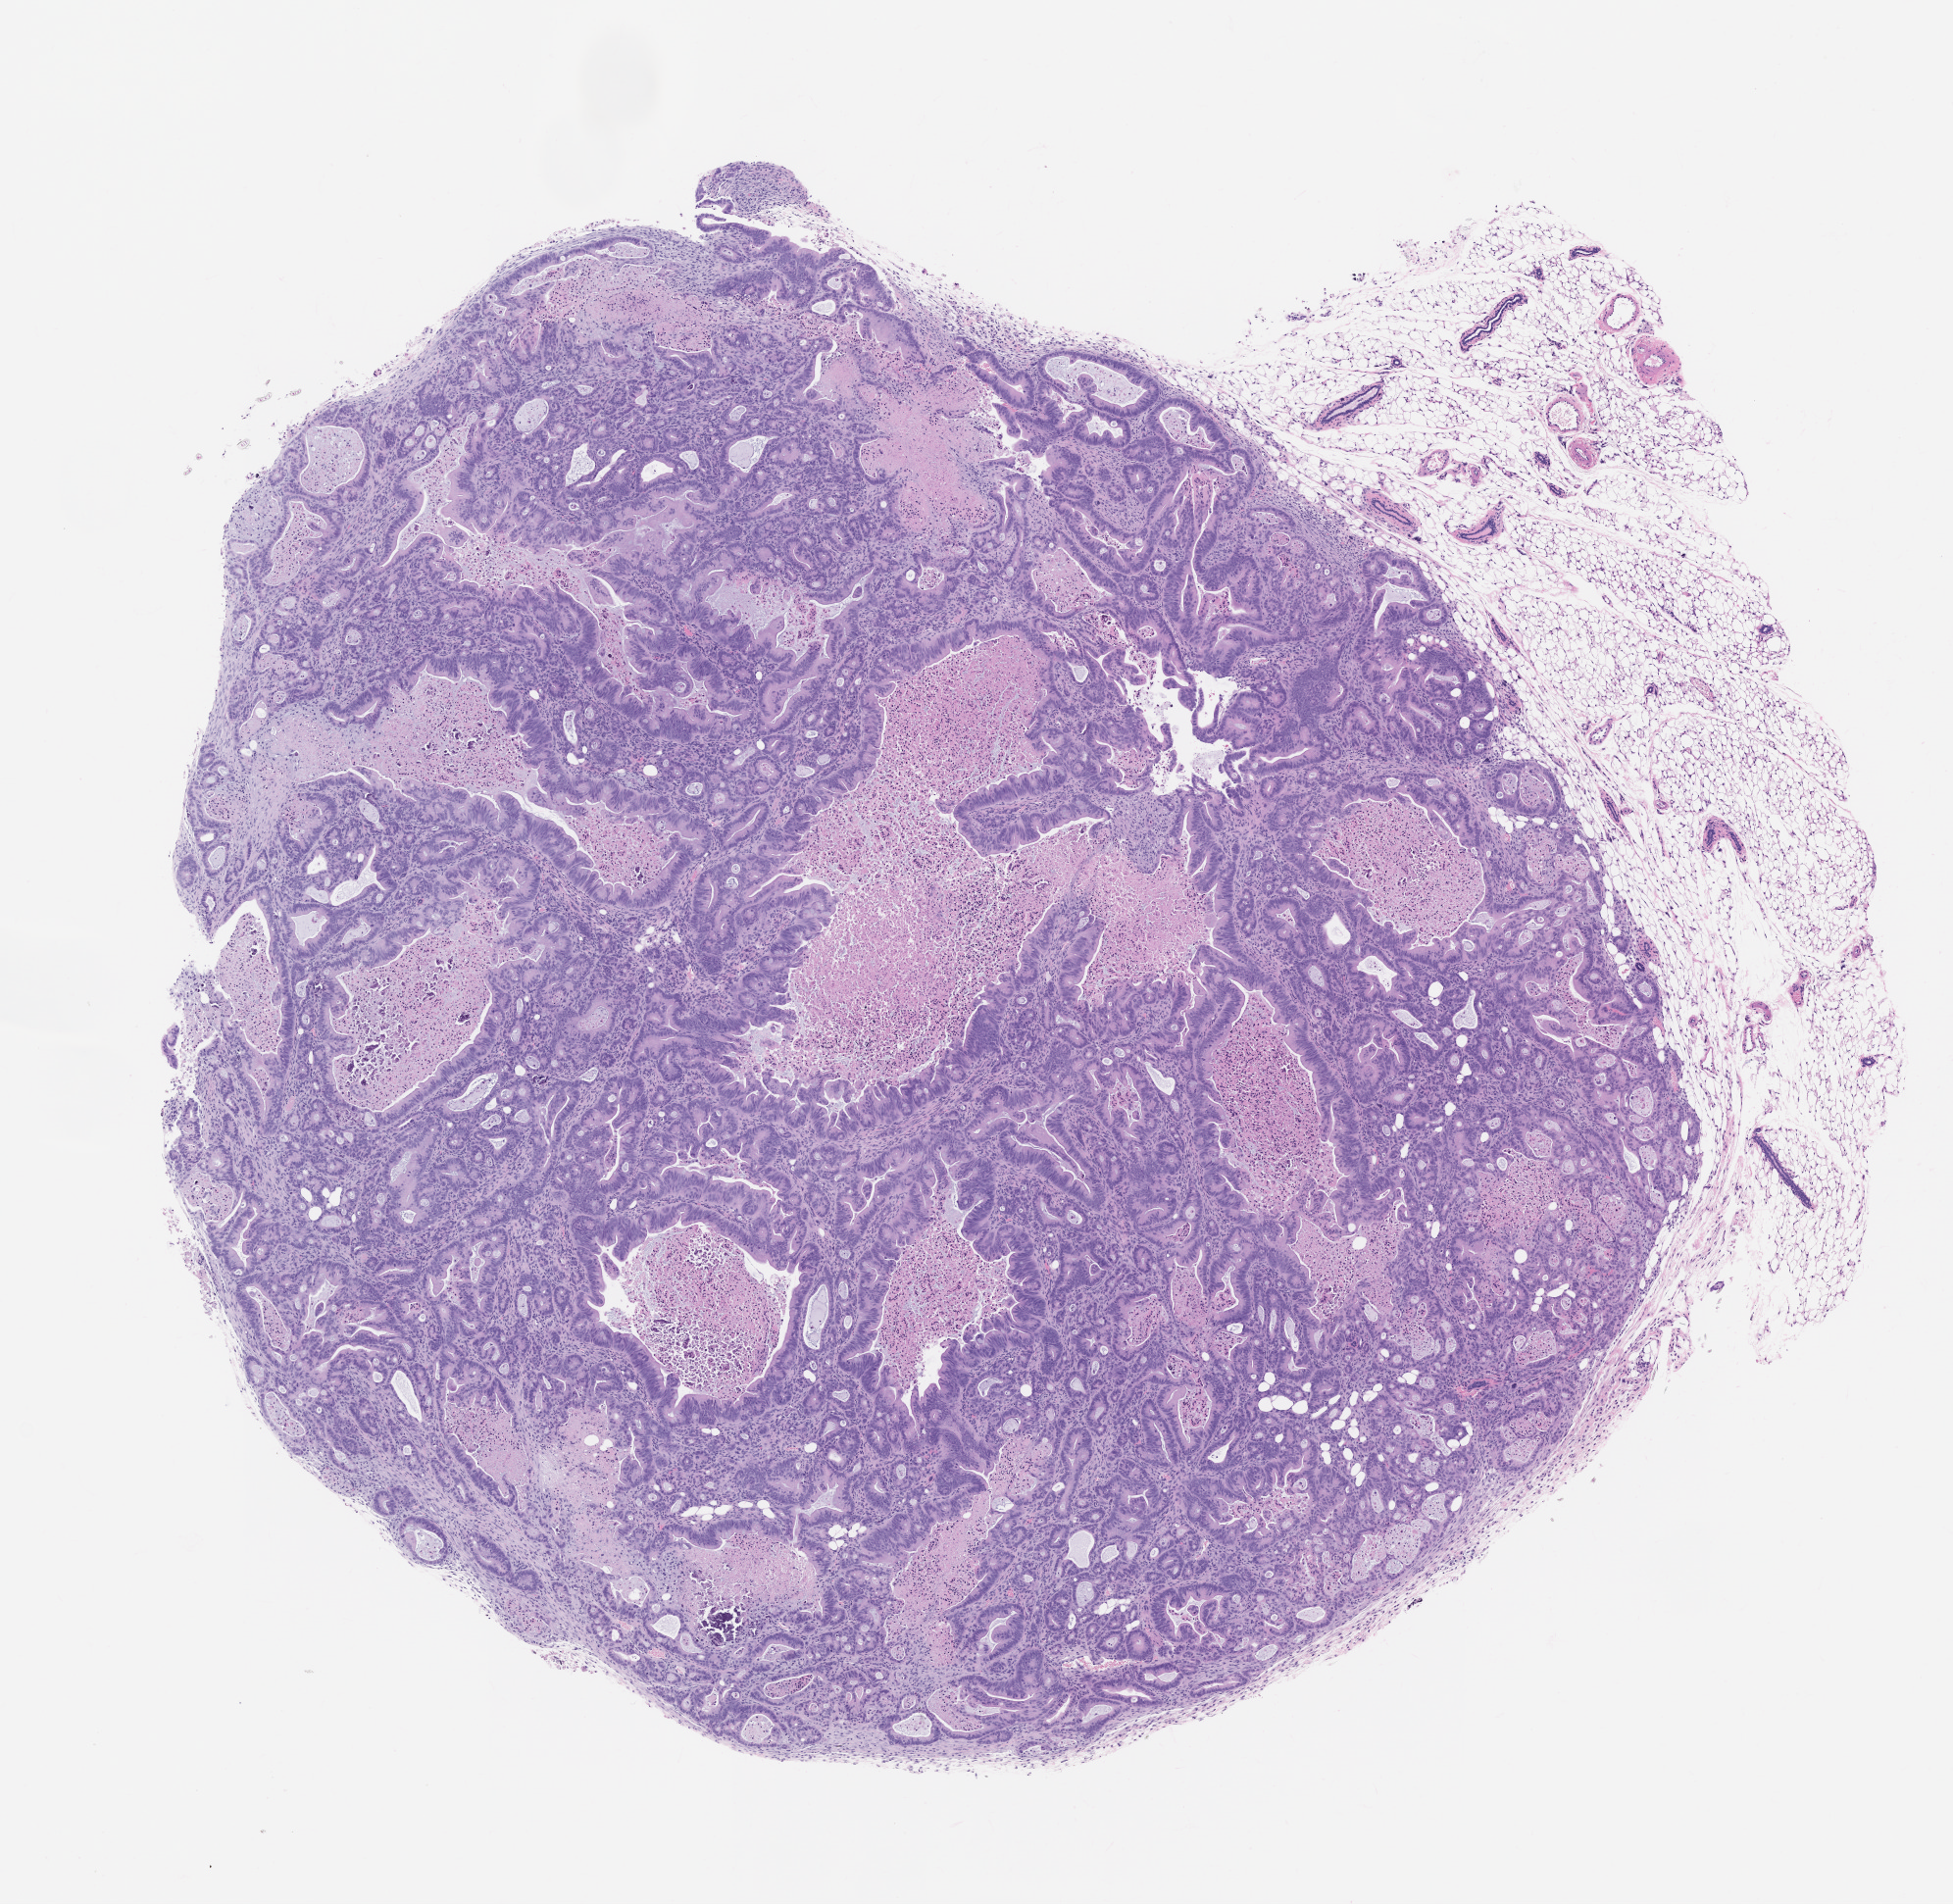
Whole-slide image, H&E: patient-derived xenograft (human tumor grown in a mouse), passage 1 — whole scanned area (about 8.0 x 7.8 mm) shown as a low-resolution overview; formalin-fixed paraffin-embedded section; originating tumor site category: colon.
• originating patient diagnosis: Colon Adenocarcinoma